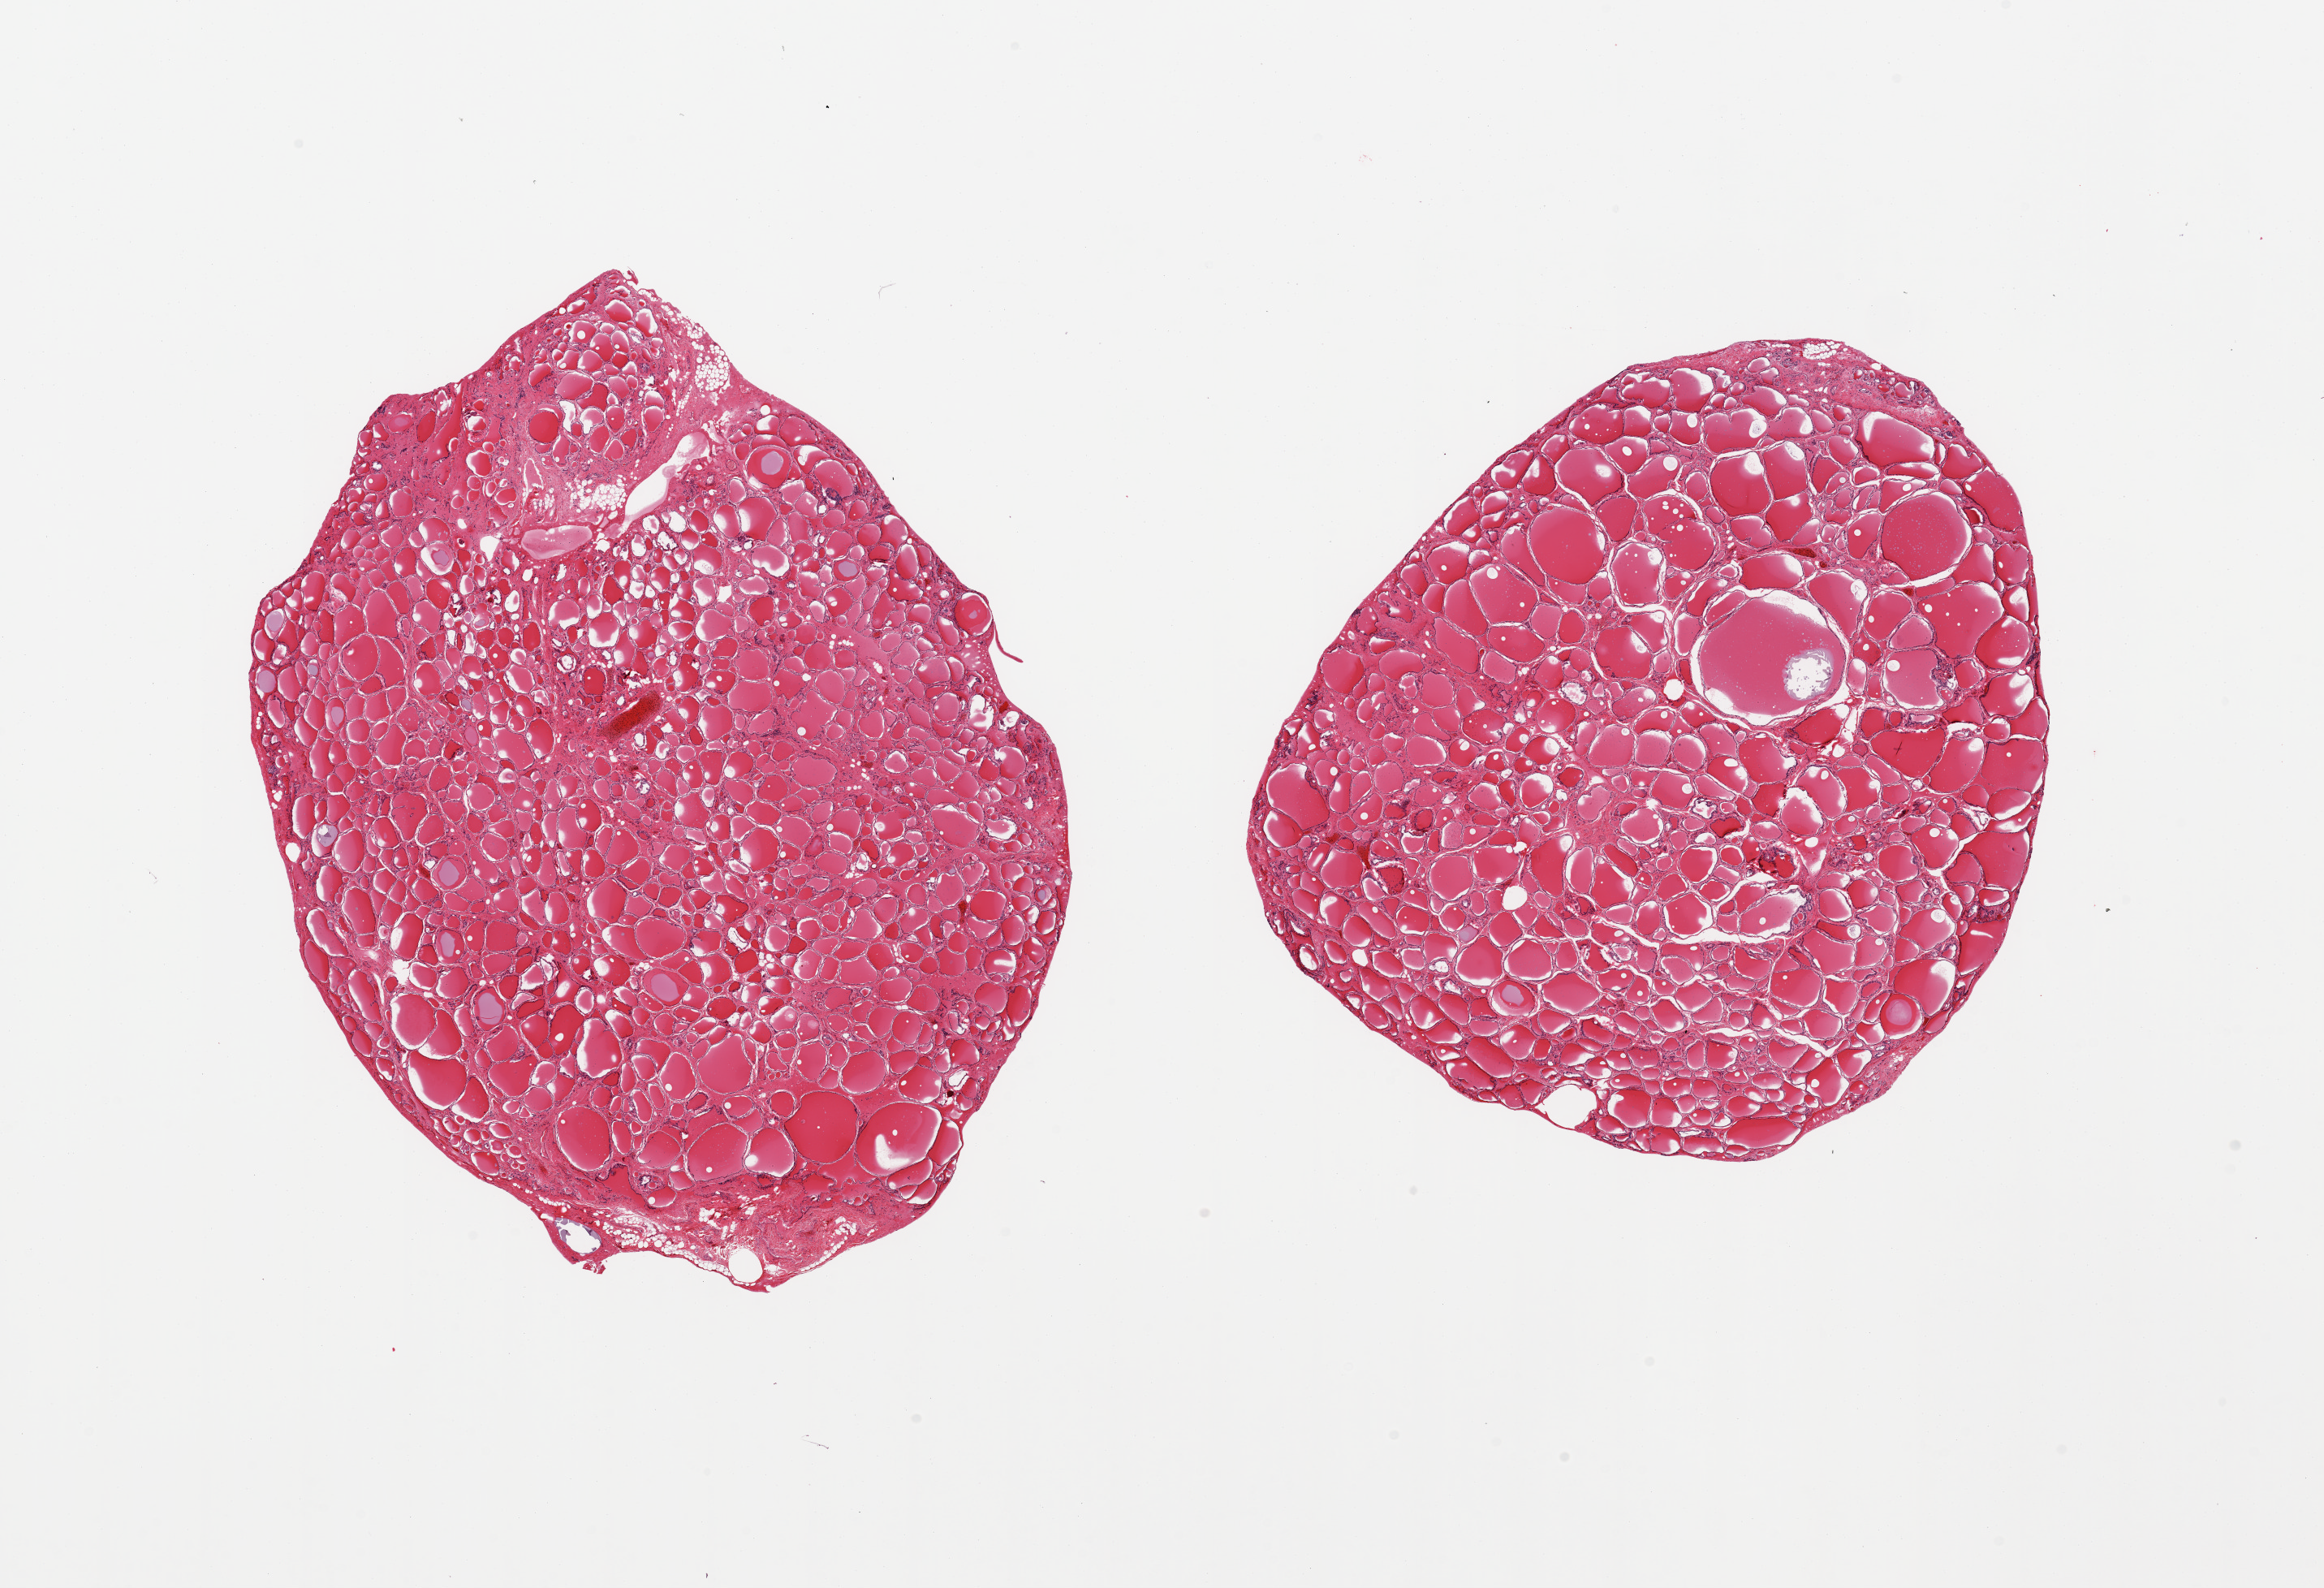
Whole-slide image, hematoxylin and eosin (H&E) stain, brightfield, shown as a low-resolution overview of the whole scanned area (about 22.6 x 15.5 mm); PAXgene-fixed, paraffin-embedded tissue; target tissue: thyroid; tissue donor sample. Male donor.
Pathologist's review note for this sample: 2 pieces; well dissected.